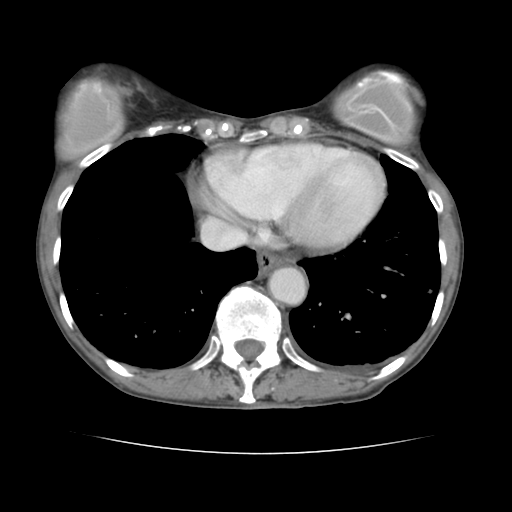
Contrast-enhanced abdominal CT, one axial slice; position 135 of 136 along the scan axis; 120 kVp; soft-tissue window (W 400 / L 40 HU); 2.5 mm slice thickness; 512 × 512 image matrix, field of view 319 × 319 mm. Female patient, age 77 years. Case-level facts recorded for this patient, not image findings: diagnosis: colorectal cancer liver metastases, imaged before liver resection; multiple liver metastases: yes; largest metastasis: 3 cm; disease in both lobes: no.
Outlined on this slice (expert manual segmentation):
- hepatic veins: bounding box <205,232,245,247> (left, top, right, bottom; pixels)